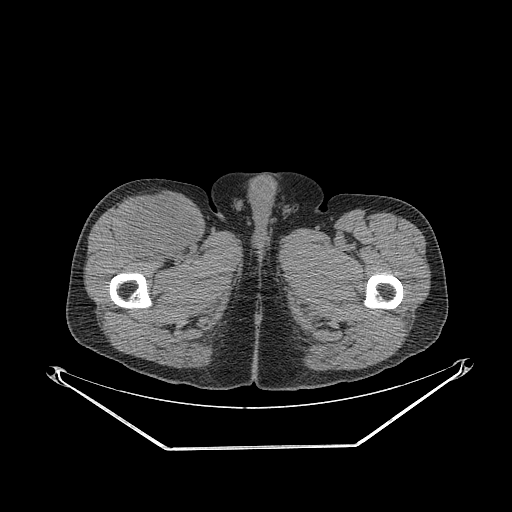
CT of an extremity soft-tissue mass (from a PET/CT study), one axial slice. Position 299 of 311 along the scan axis. Reconstruction kernel STANDARD. Soft-tissue window (W 400 / L 40 HU). 3.75 mm slice thickness. 512 × 512 image matrix. Male patient. Case-level facts recorded for this patient, not image findings: histological type: pleiomorphic leiomyosarcoma; grade: intermediate; site of the primary tumour: right thigh.
Annotated regions visible in this slice (expert contour drawn on MRI and transferred to this co-registered scan by the dataset authors):
- gross tumour volume including surrounding oedema: bounding box <126,194,199,257> (left, top, right, bottom; pixels)
- gross tumour volume (mass): <128,196,199,257>